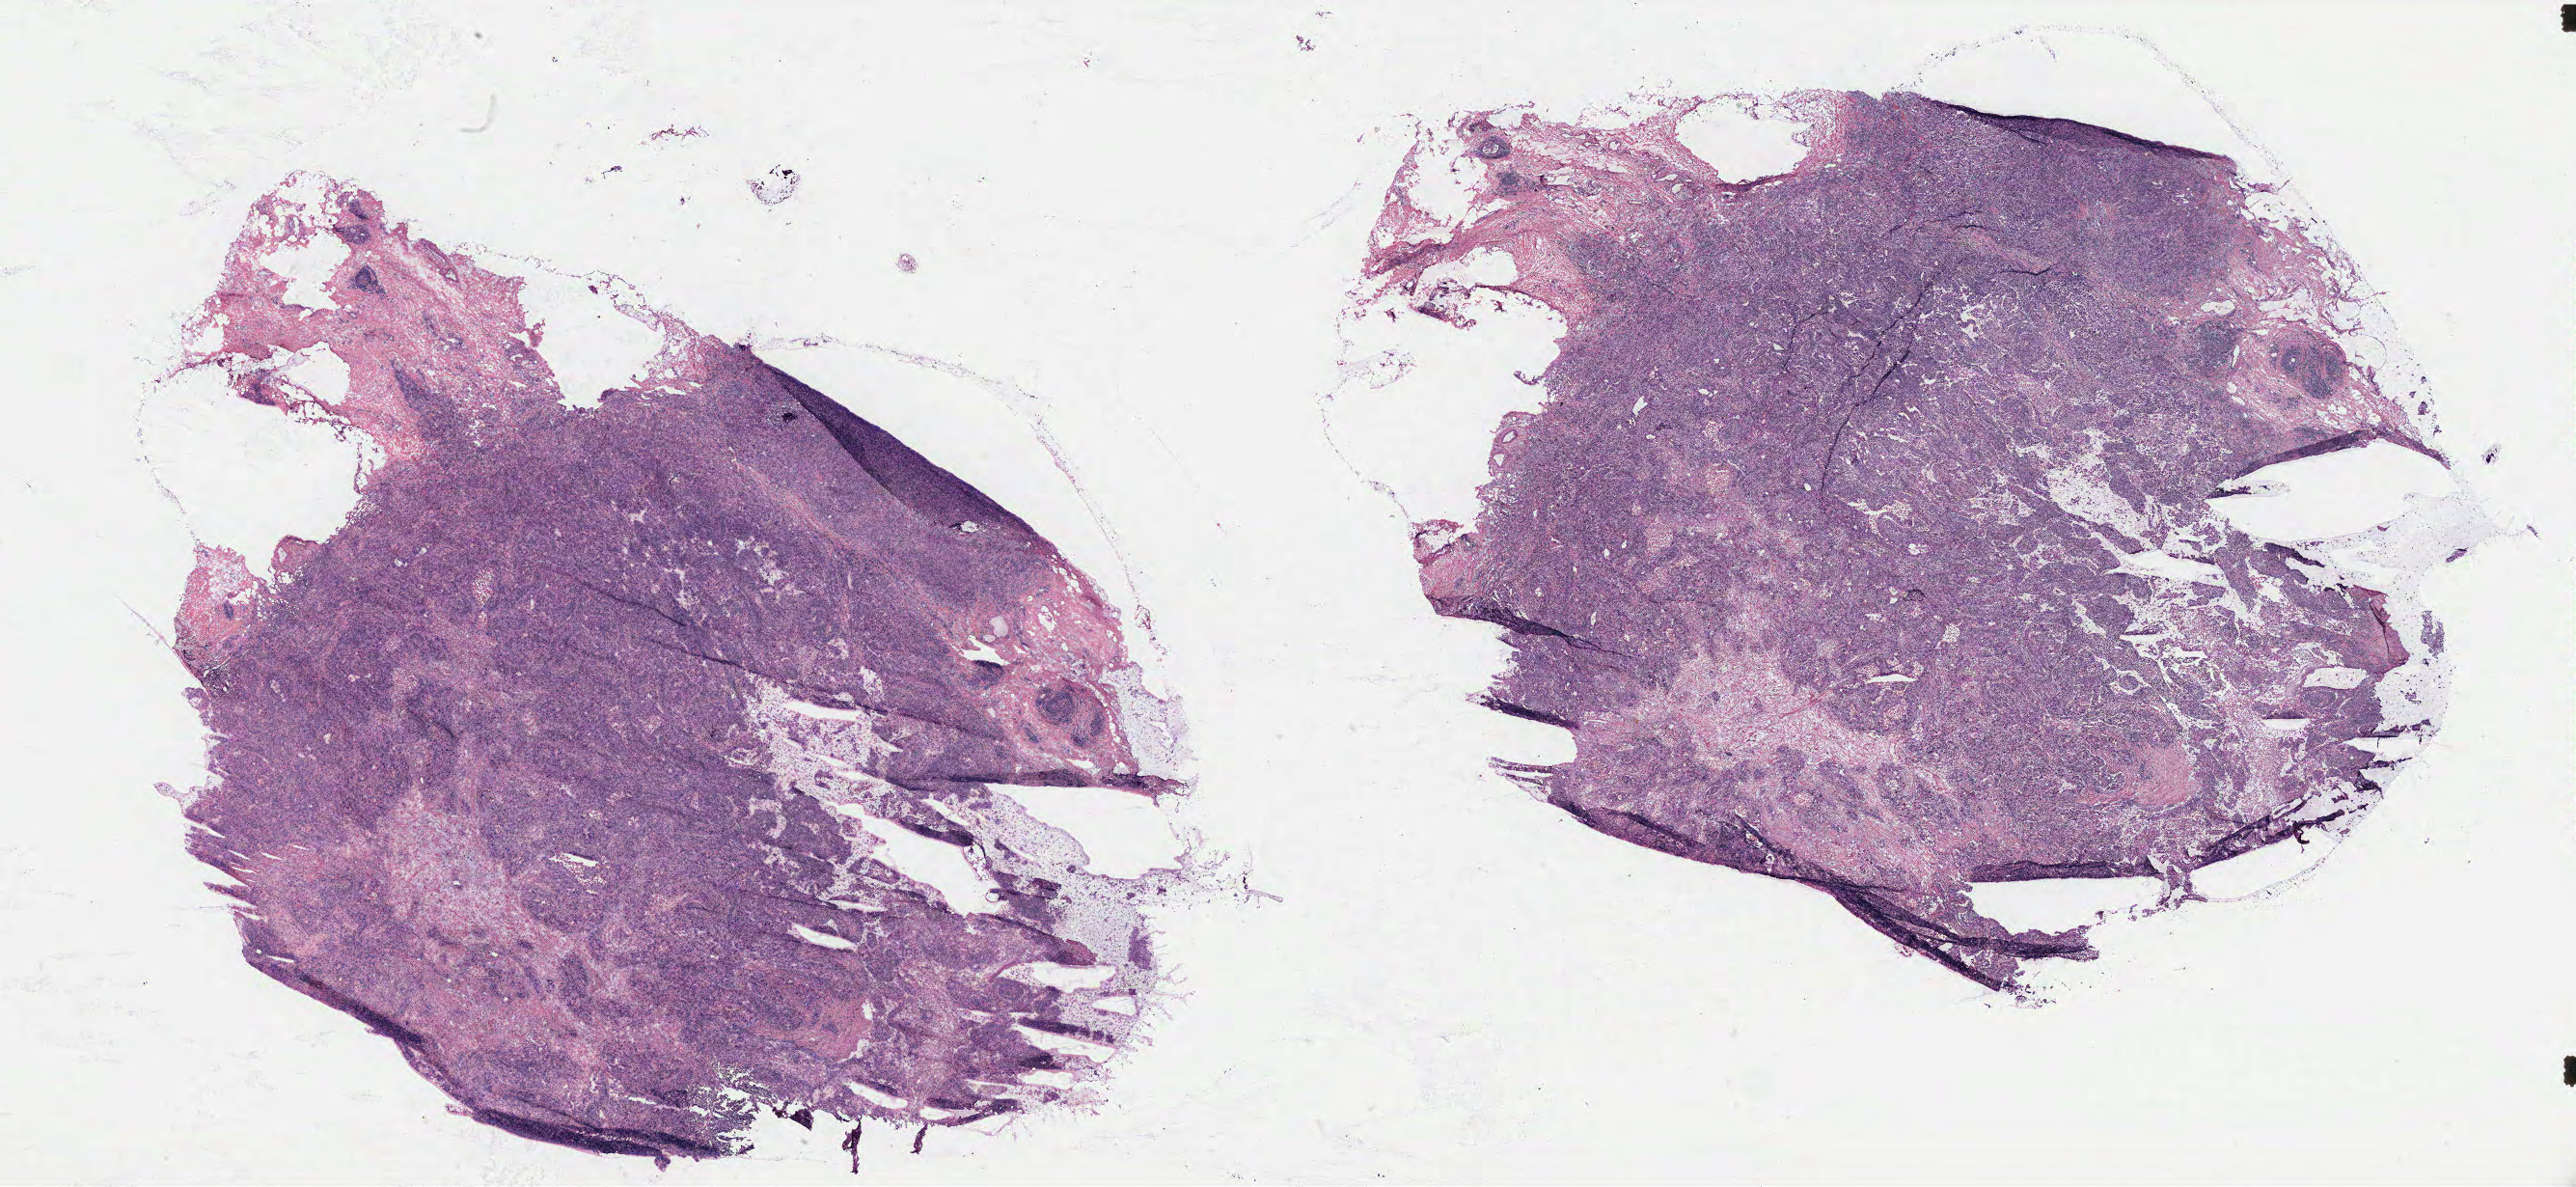
Whole-slide histology image, H&E-stained — whole scanned area (about 42.7 x 19.7 mm) shown as a low-resolution overview; breast, tissue type not recorded. Female, 74 y/o.
• patient diagnosis: Infiltrating duct carcinoma, NOS